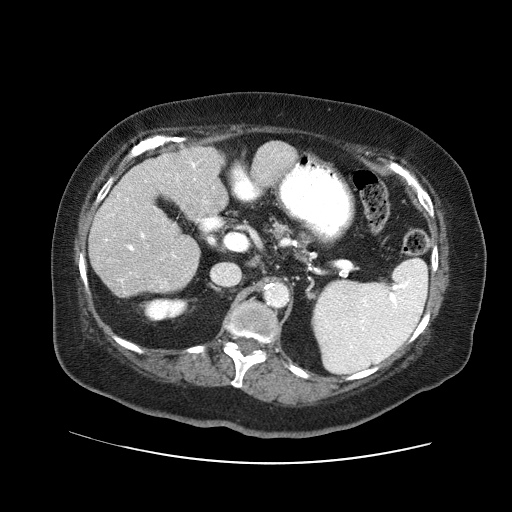
Contrast-enhanced abdominal CT (liver protocol), one axial slice; position 23 of 71 along the scan axis; reconstruction kernel STANDARD; soft-tissue window (W 400 / L 40 HU); 2.5 mm slice thickness; 512 × 512 image matrix, field of view 400 × 400 mm. From the clinical record (not read from this slice): diagnosis: hepatocellular carcinoma (patient treated with transarterial chemoembolisation; whether this scan precedes or follows treatment is not stated here); TNM stage (as recorded): Stage-II; Child-Pugh class: A; tumour differentiation: poorly differentiated; tumour nodularity: multinodular.
Annotated regions visible in this slice (semi-automatic segmentation, software-assisted and operator-edited):
- liver parenchyma outside the tumour (the mass and vessels are separate outlines, so this box may not span the whole liver): bounding box <88,142,296,296> (left, top, right, bottom; pixels)
- liver vessels: <105,162,207,282>